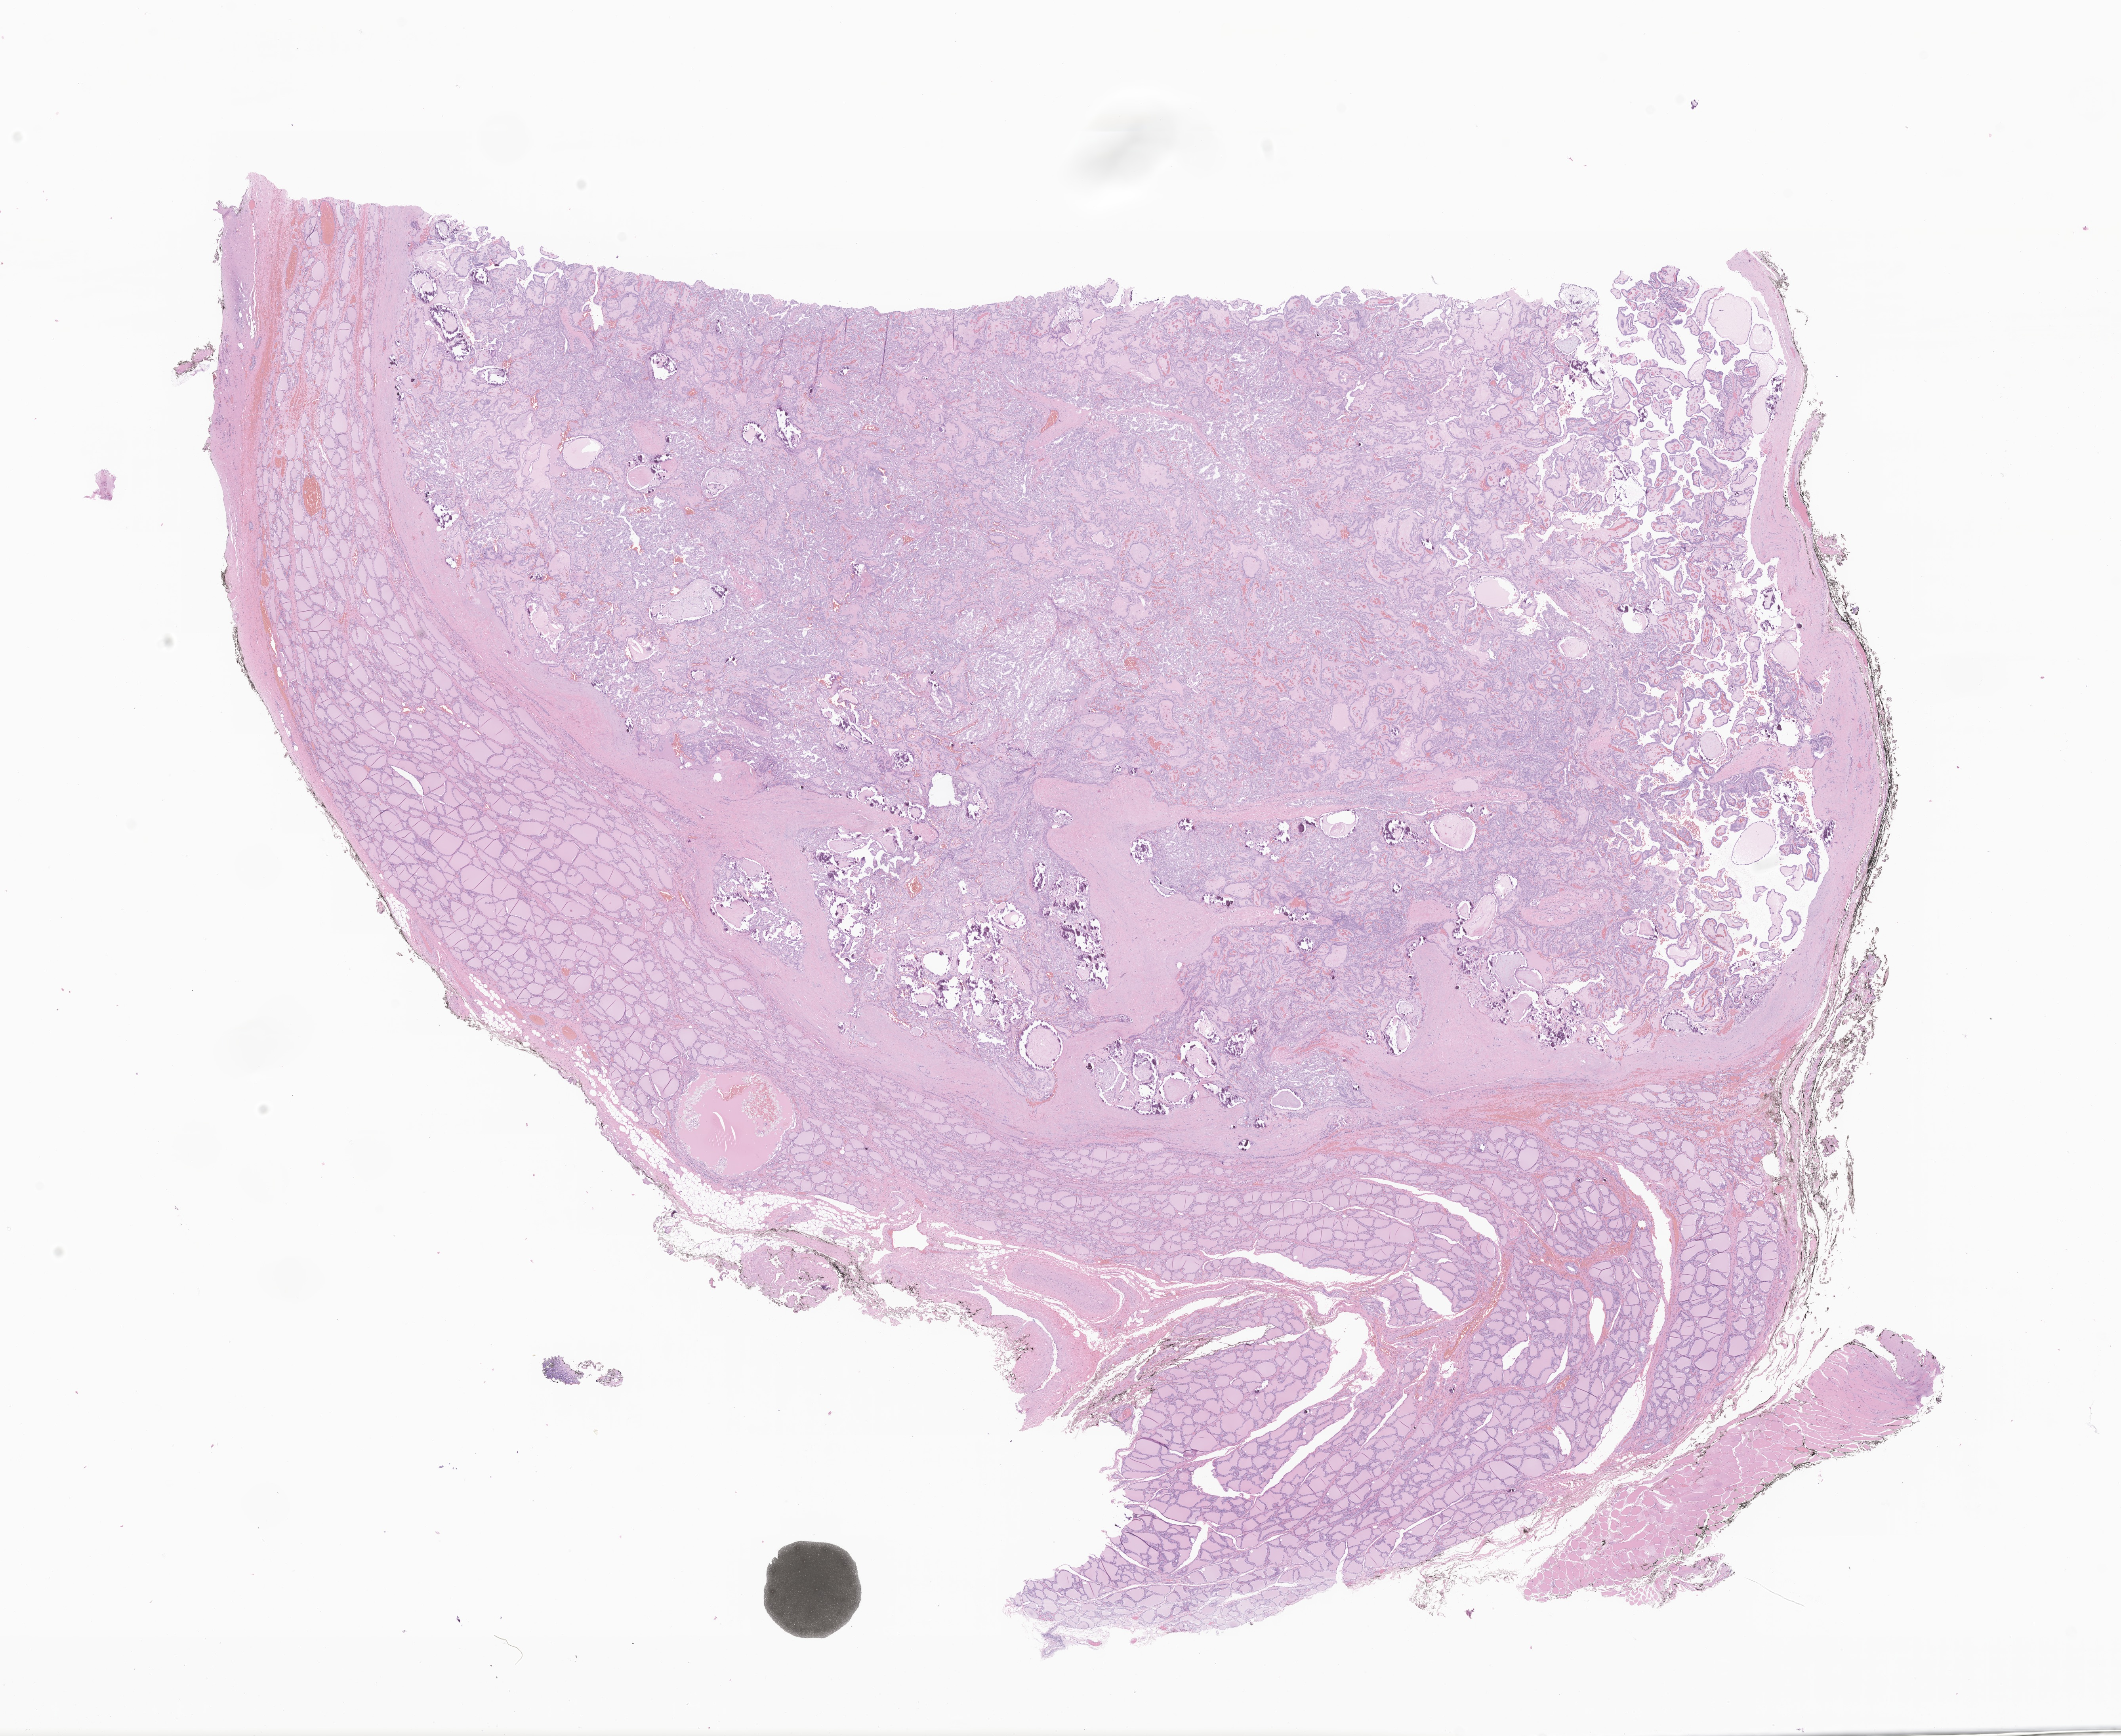
H&E whole-slide image of tumor tissue from the thyroid — shown as a low-resolution overview of the whole scanned area (about 22.6 x 18.5 mm). Formalin-fixed, paraffin-embedded (FFPE) tissue. Female patient, age 171 months (14 years 3 months).
Diagnosis: Papillary carcinoma, NOS.